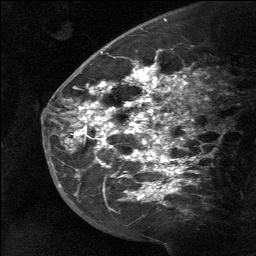
Breast MRI (dynamic contrast-enhanced), one sagittal slice. Slice 42 of 64 in the series (ordered by position). Dynamic contrast-enhanced study with each time point stored as its own series, time point 2 of 3 at this slice position (early post-contrast, ordered by acquisition time). 1.5 T. TE 4.8 ms, TR 27 ms. 256 × 256 image matrix. Patient: female, 39 years. From the clinical record (not read from this slice): setting: breast cancer imaged before/during neoadjuvant chemotherapy; receptor status: HER2-positive.
Annotated regions visible in this slice (semi-automatically segmented with operator editing):
- analysis volume of interest (the breast-tissue region the enhancement analysis was run in; not a lesion): bounding box <58,40,198,217> (left, top, right, bottom; pixels)
- tumour enhancement mask (voxels above the 90 % enhancement threshold inside the analysis volume of interest): <74,63,177,200>